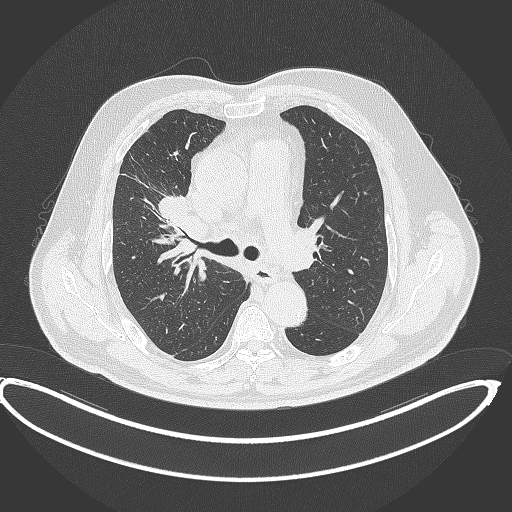
Chest CT, one axial slice; slice 262 of 390 in the series (ordered by position); lung window (W 1500 / L -600 HU); 1 mm slice thickness; 512 × 512 image matrix, field of view 448 × 448 mm. Patient: male, 62 years. Case-level facts recorded for this patient, not image findings: clinical TNM (as recorded): T1c N3 M1c.
Annotated regions visible in this slice (bounding box drawn by a radiologist):
- lung tumour (recorded histology: adenocarcinoma): bounding box <154,196,198,236> (left, top, right, bottom; pixels)